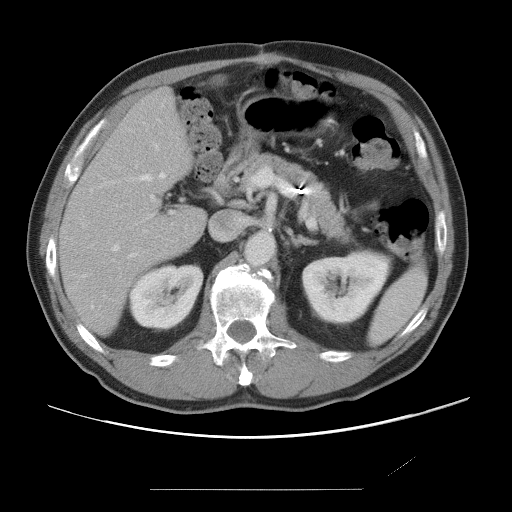
Contrast-enhanced abdominal CT, one axial slice; position 38 of 87 along the scan axis; 120 kVp; intravenous contrast given; soft-tissue window (W 400 / L 40 HU); 512 × 512 image matrix. Male patient, age 74 years. Case-level facts recorded for this patient, not image findings: diagnosis: colorectal cancer liver metastases, imaged before liver resection; multiple liver metastases: yes; largest metastasis: 1.1 cm; disease in both lobes: no.
Annotated regions visible in this slice (outlined manually by an expert reader):
- hepatic veins: bounding box [x1, y1, x2, y2] px = [91, 145, 165, 308]
- liver: [62, 89, 206, 331]
- planned liver remnant (the part of the liver to remain after resection): [62, 89, 206, 331]
- portal vein (with intrahepatic branches): [136, 166, 274, 217]